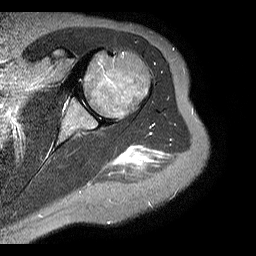
MRI of an extremity soft-tissue mass, one axial slice. Slice 13 of 20 in the series (ordered by position). STIR. 4 mm slice thickness. 256 × 256 image matrix, field of view 150 × 150 mm. Female patient. From the clinical record (not read from this slice): histological type: malignant fibrous histiocytoma; grade: low; site of the primary tumour: left arm.
Outlined on this slice (manually delineated by an expert):
- gross tumour volume (mass): bounding box (x1, y1, x2, y2) in pixels: (119, 145, 145, 164)